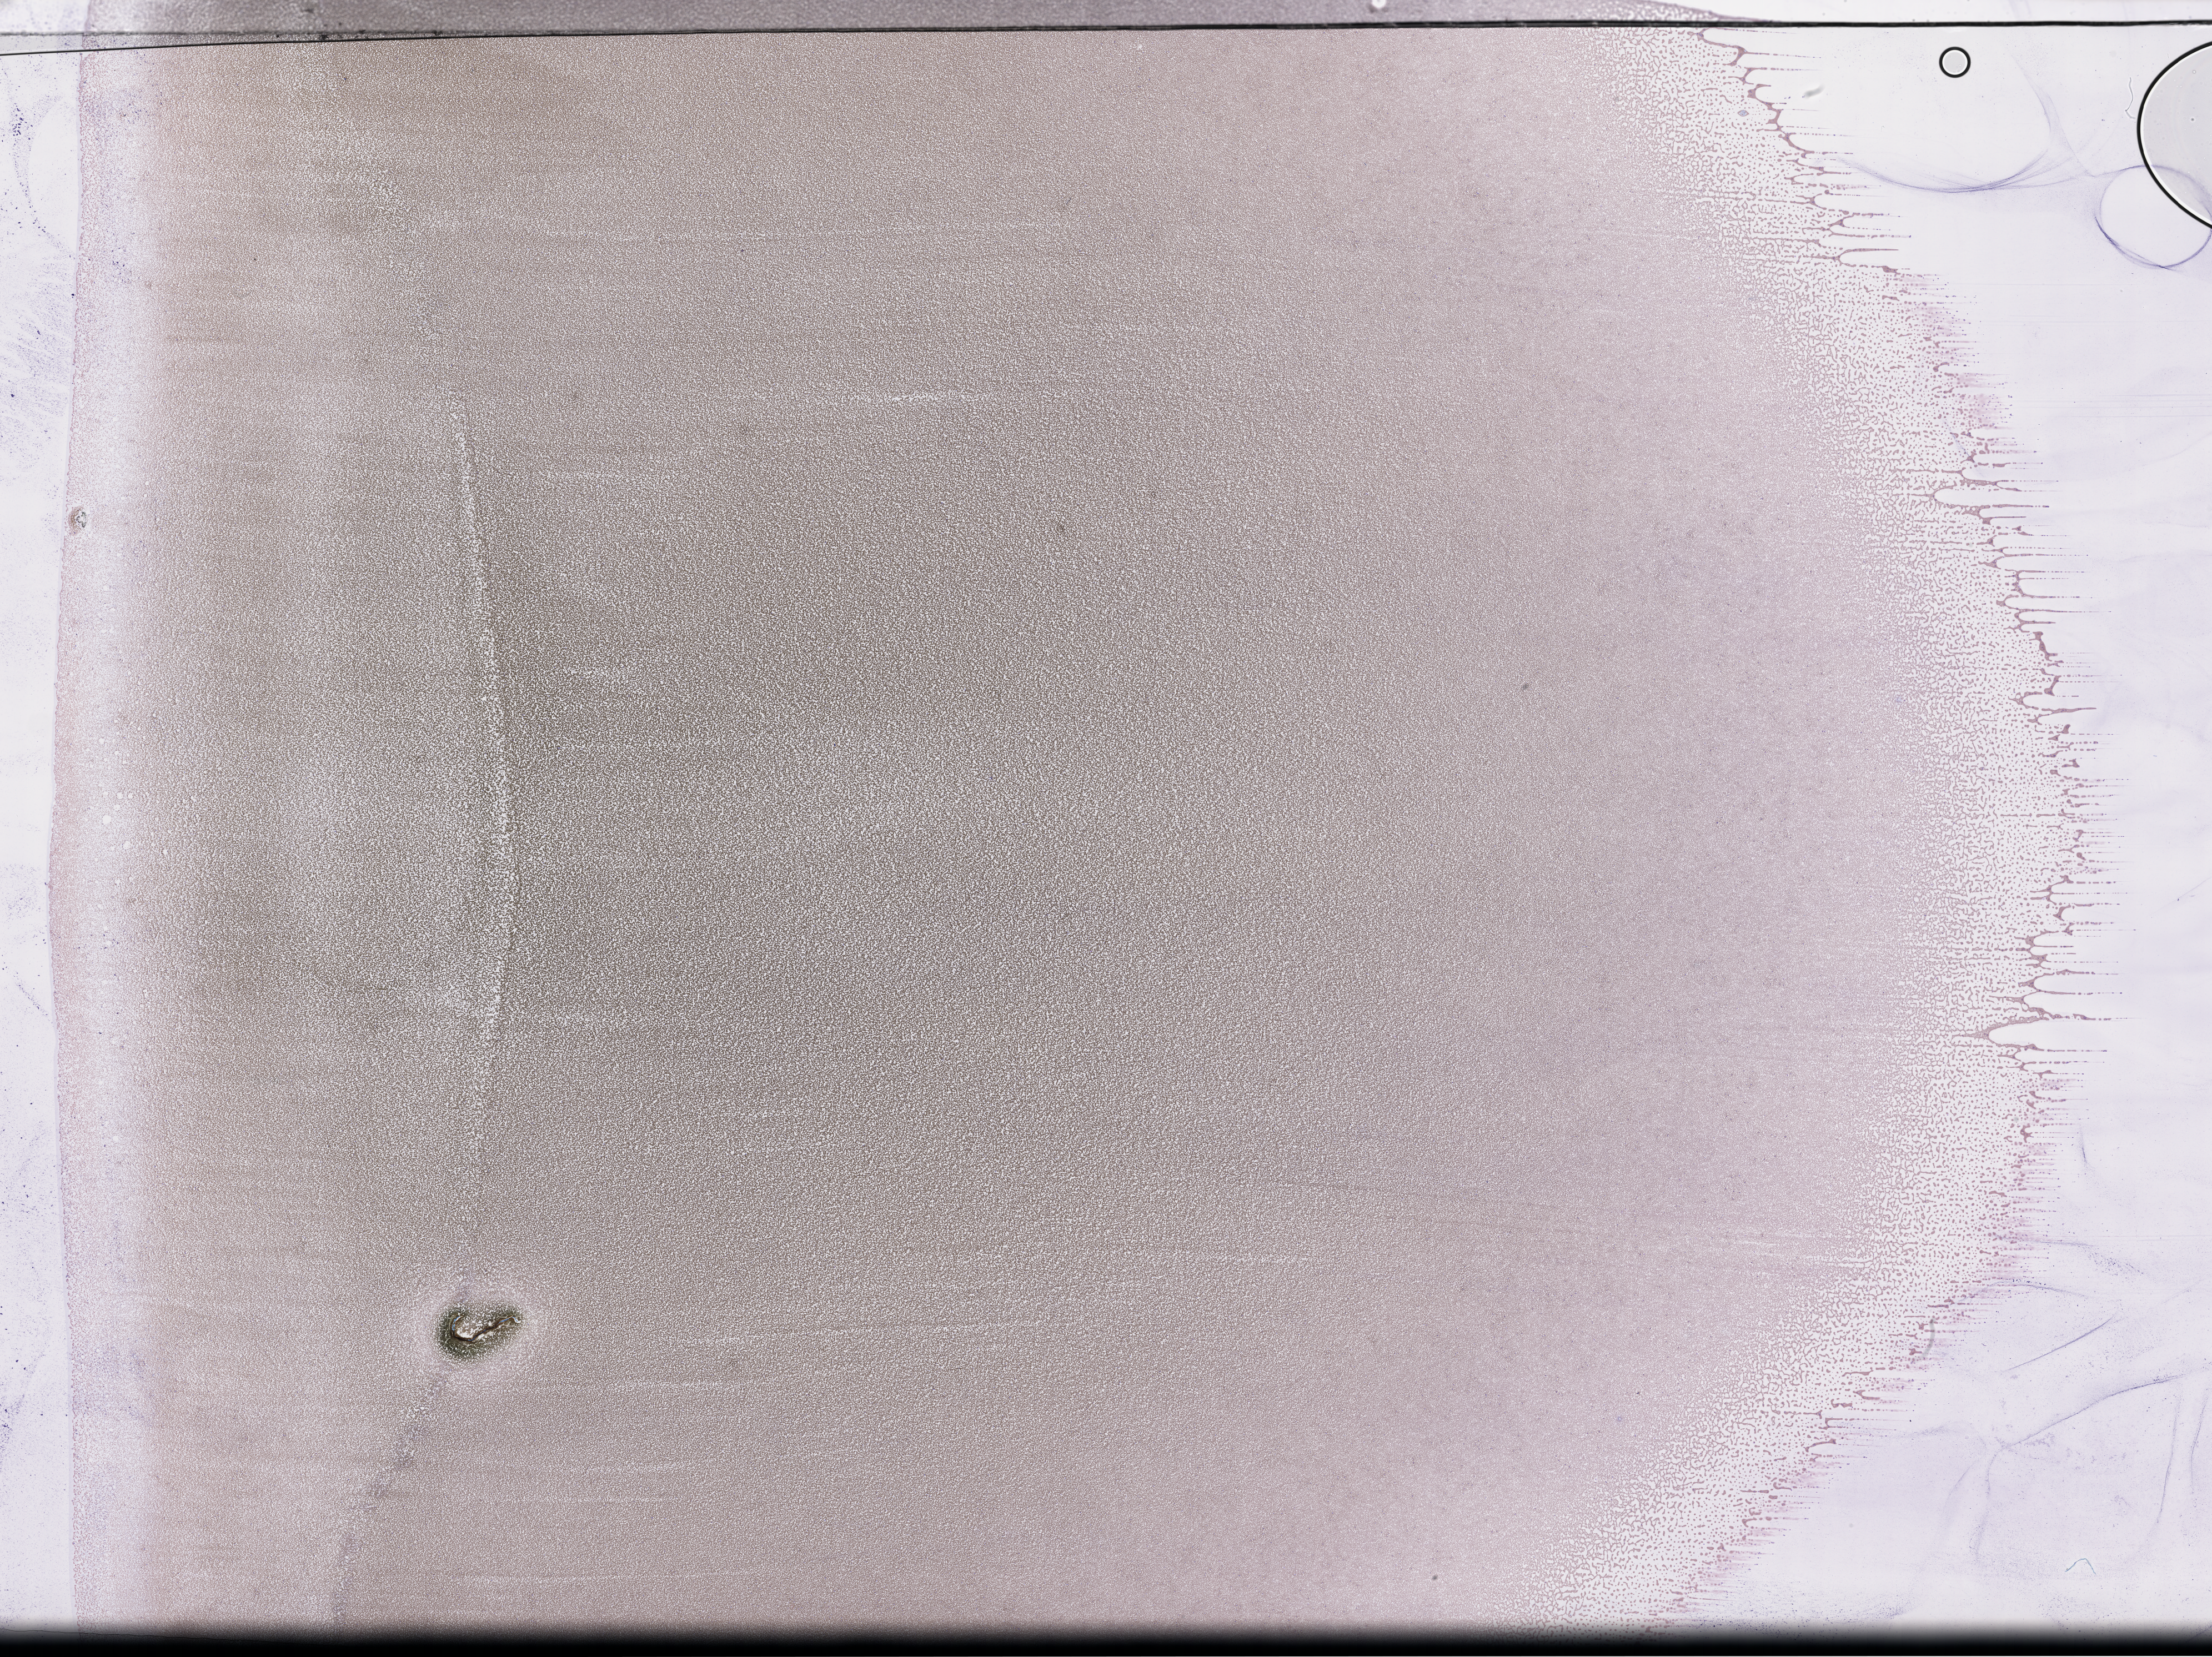
Wright-Giemsa-stained whole blood smear, whole-slide image — whole scanned area (about 32.2 x 24.1 mm) shown as a low-resolution overview; smear from an EDTA sample; collected on treatment. Patient: female.
From a patient with: Plasma Cell Myeloma.